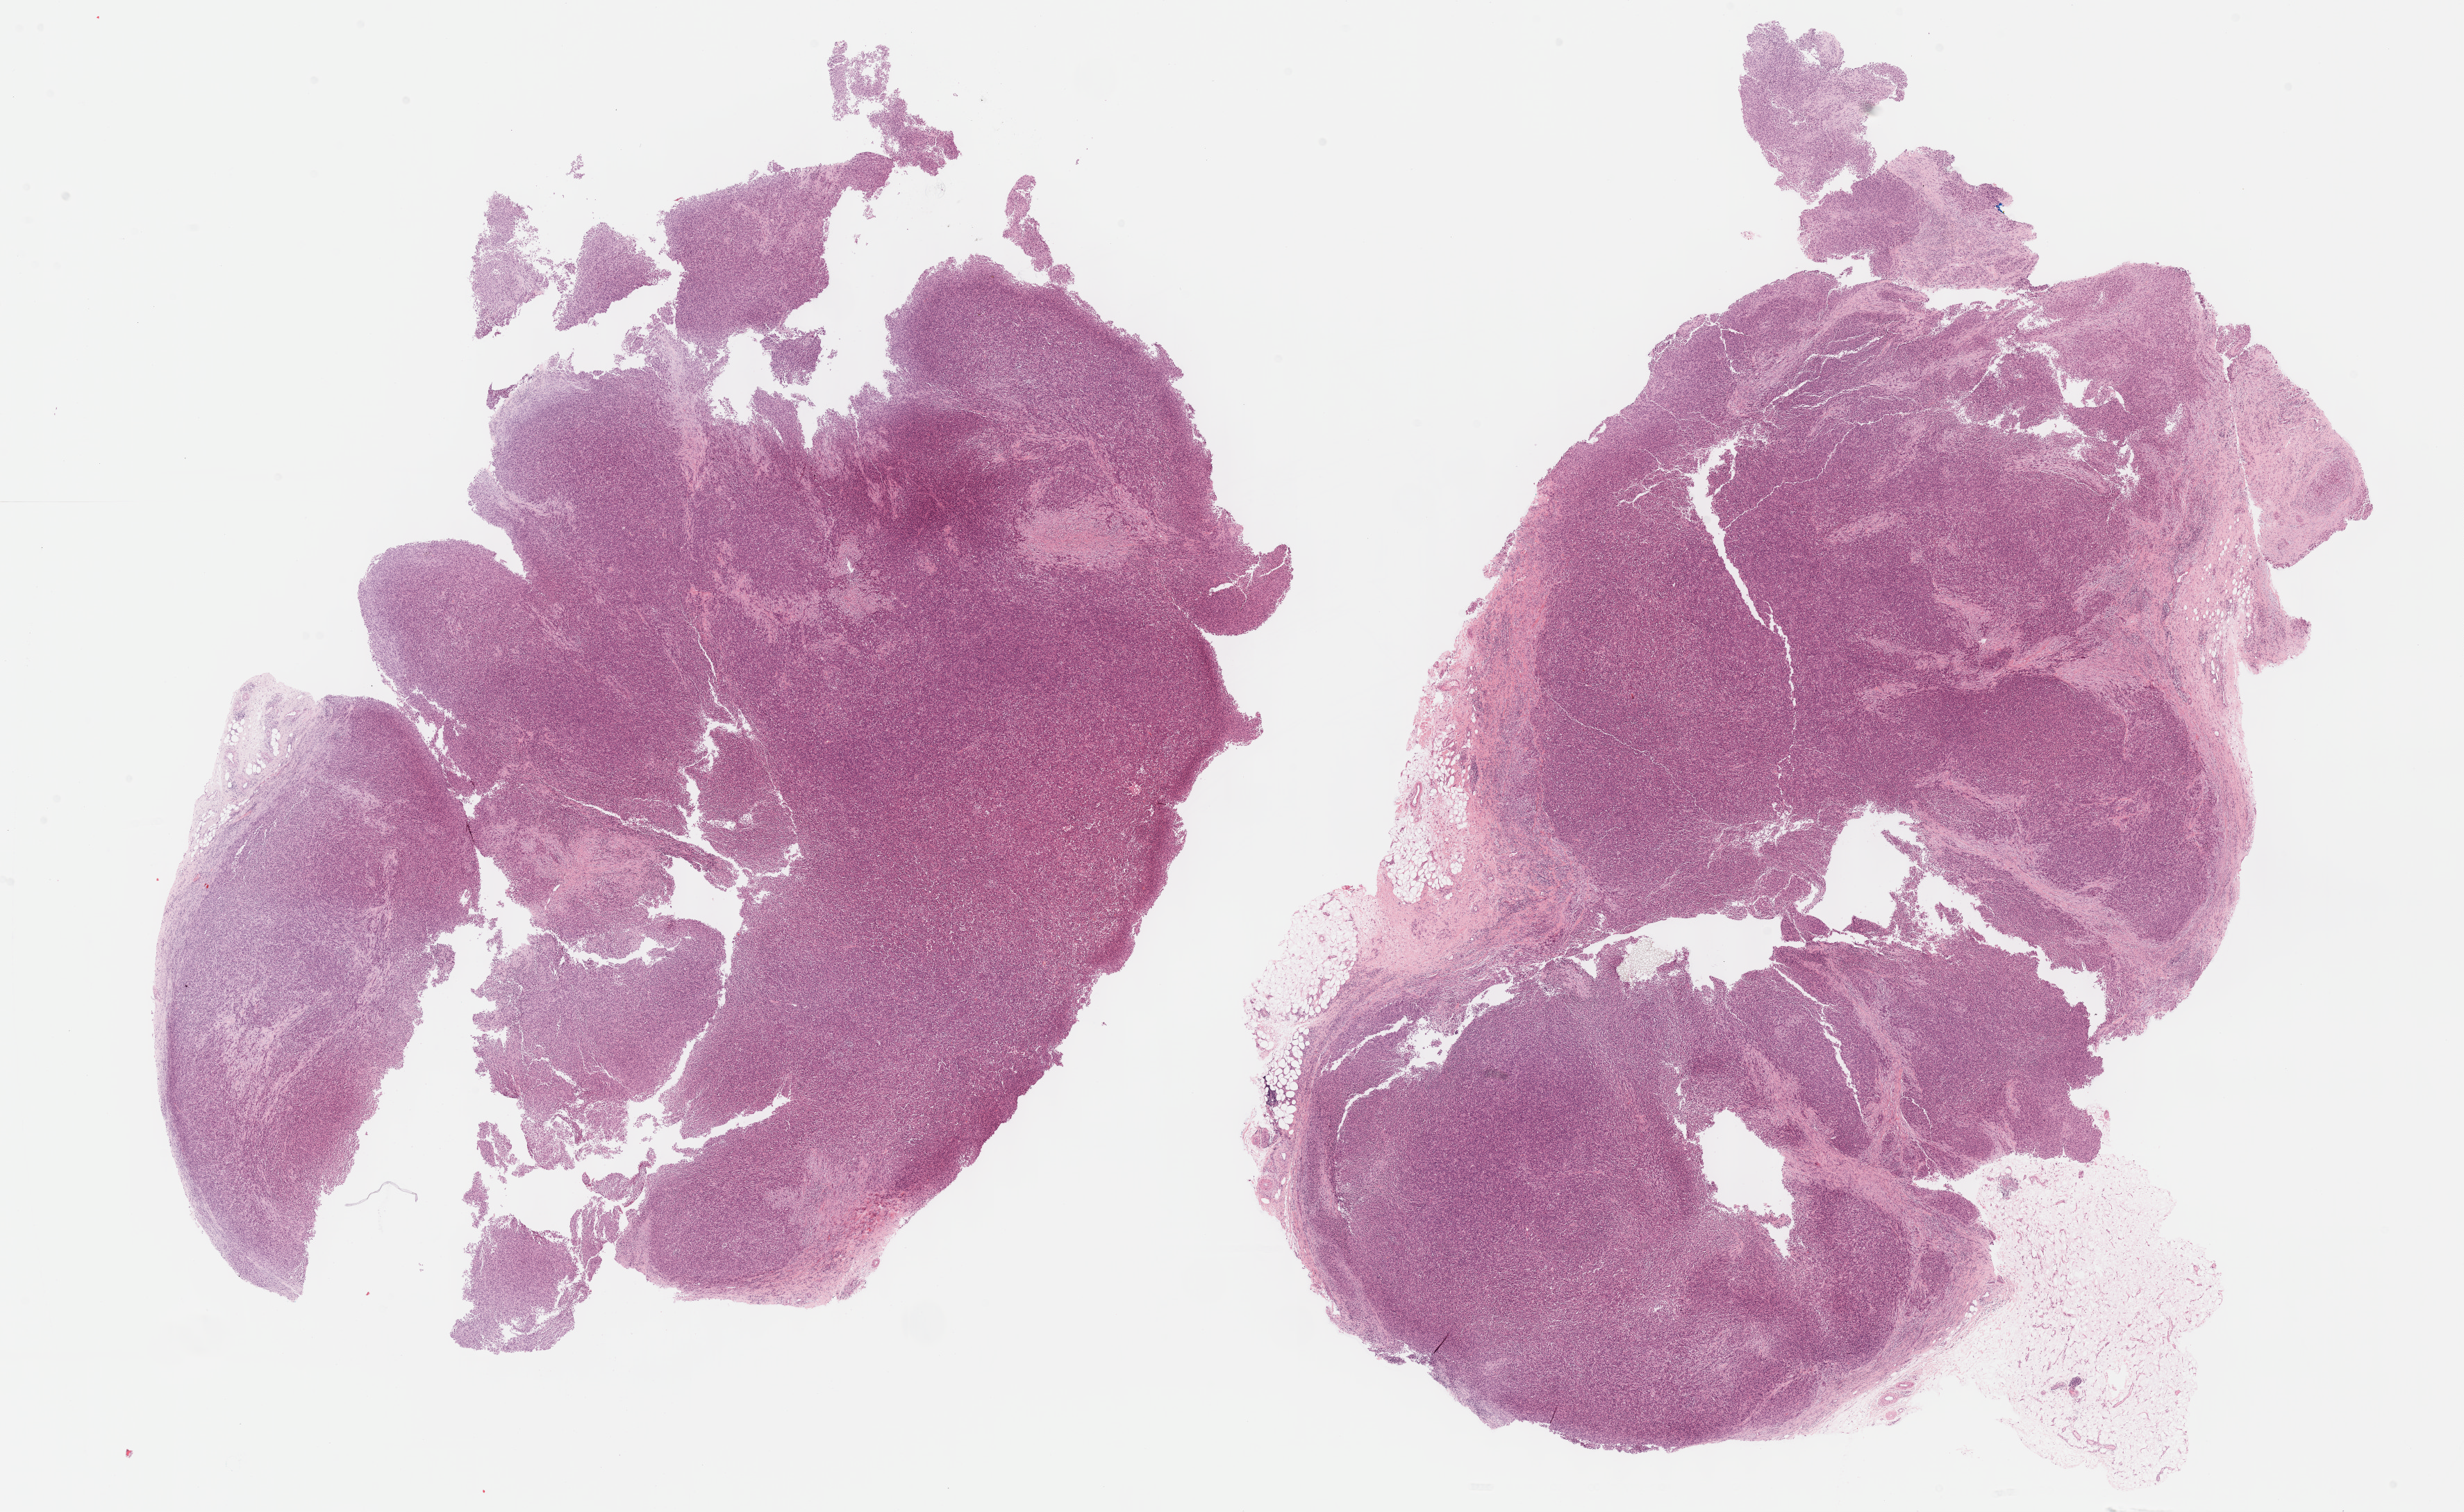
Digitized H&E tissue section (whole slide), a low-resolution overview of the entire scanned area, about 28.7 x 17.6 mm (acquisition: 40x scan), formalin-fixed paraffin-embedded (FFPE) diagnostic section, metastatic tumour sample. Patient: male, age at initial diagnosis 65 years.
This section: metastatic tumour tissue. Patient diagnosis: Lentigo maligna melanoma.